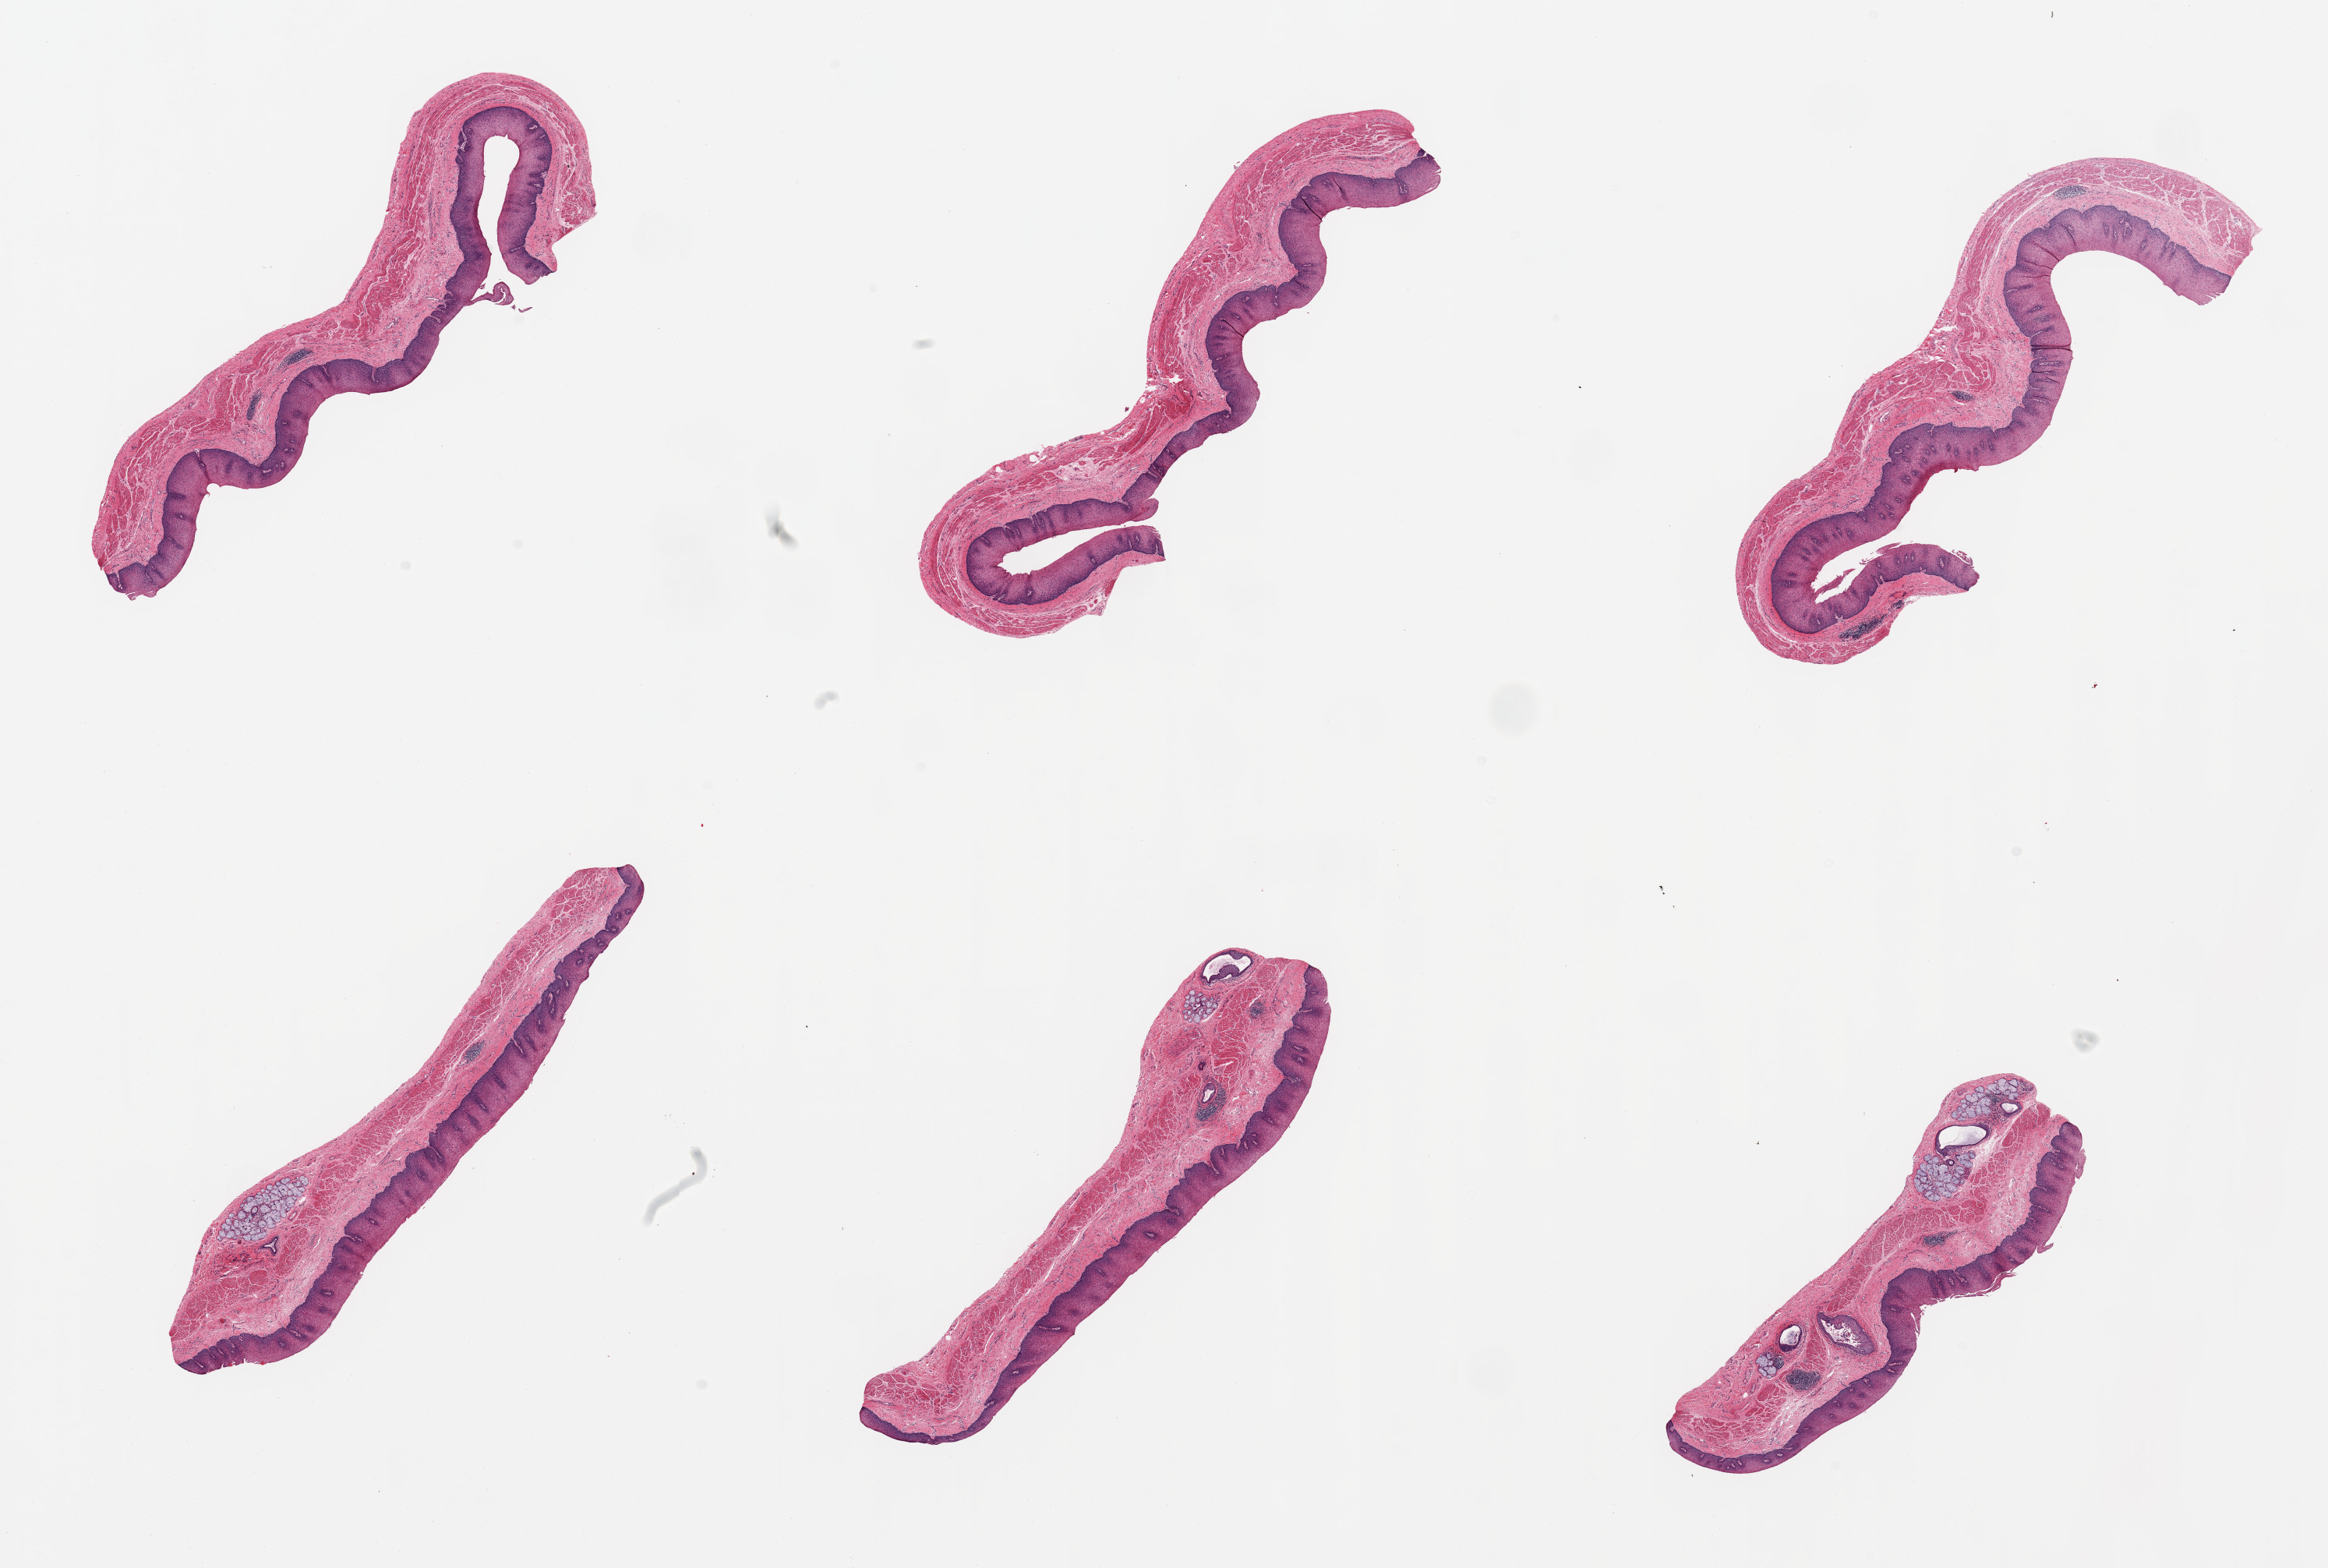
Whole-slide image, H&E stain, shown as a low-resolution overview of the whole scanned area (about 23.6 x 15.9 mm, slide scanned at 20x), PAXgene-fixed paraffin-embedded (PFPE) section, section of esophageal mucous membrane (target tissue), tissue donor sample. Male donor.
Pathologist's review note for this sample: 6 pieces; in 2 pieces prominent submucosal glands and inflamed dilated squamous metaplastic ducts; well dissected.